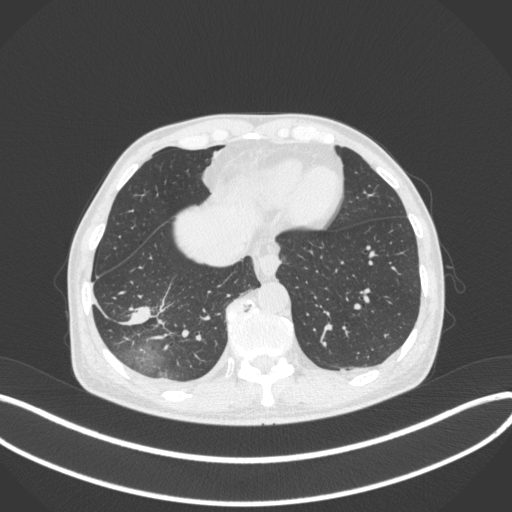
Chest CT, one axial slice. Position 92 of 385 along the scan axis. Reconstruction kernel B31f. Lung window (W 1500 / L -600 HU). 1 mm slice thickness. 512 × 512 image matrix, field of view 400 × 400 mm. Patient: male, 64 years. Case-level facts recorded for this patient, not image findings: clinical TNM (as recorded): T3 N0 M0; histopathological grade: G2-3.
Structures marked on this image (rectangle marked by the reading radiologist):
- lung tumour (recorded histology: adenocarcinoma): bounding box [x1, y1, x2, y2] px = [121, 297, 157, 329]